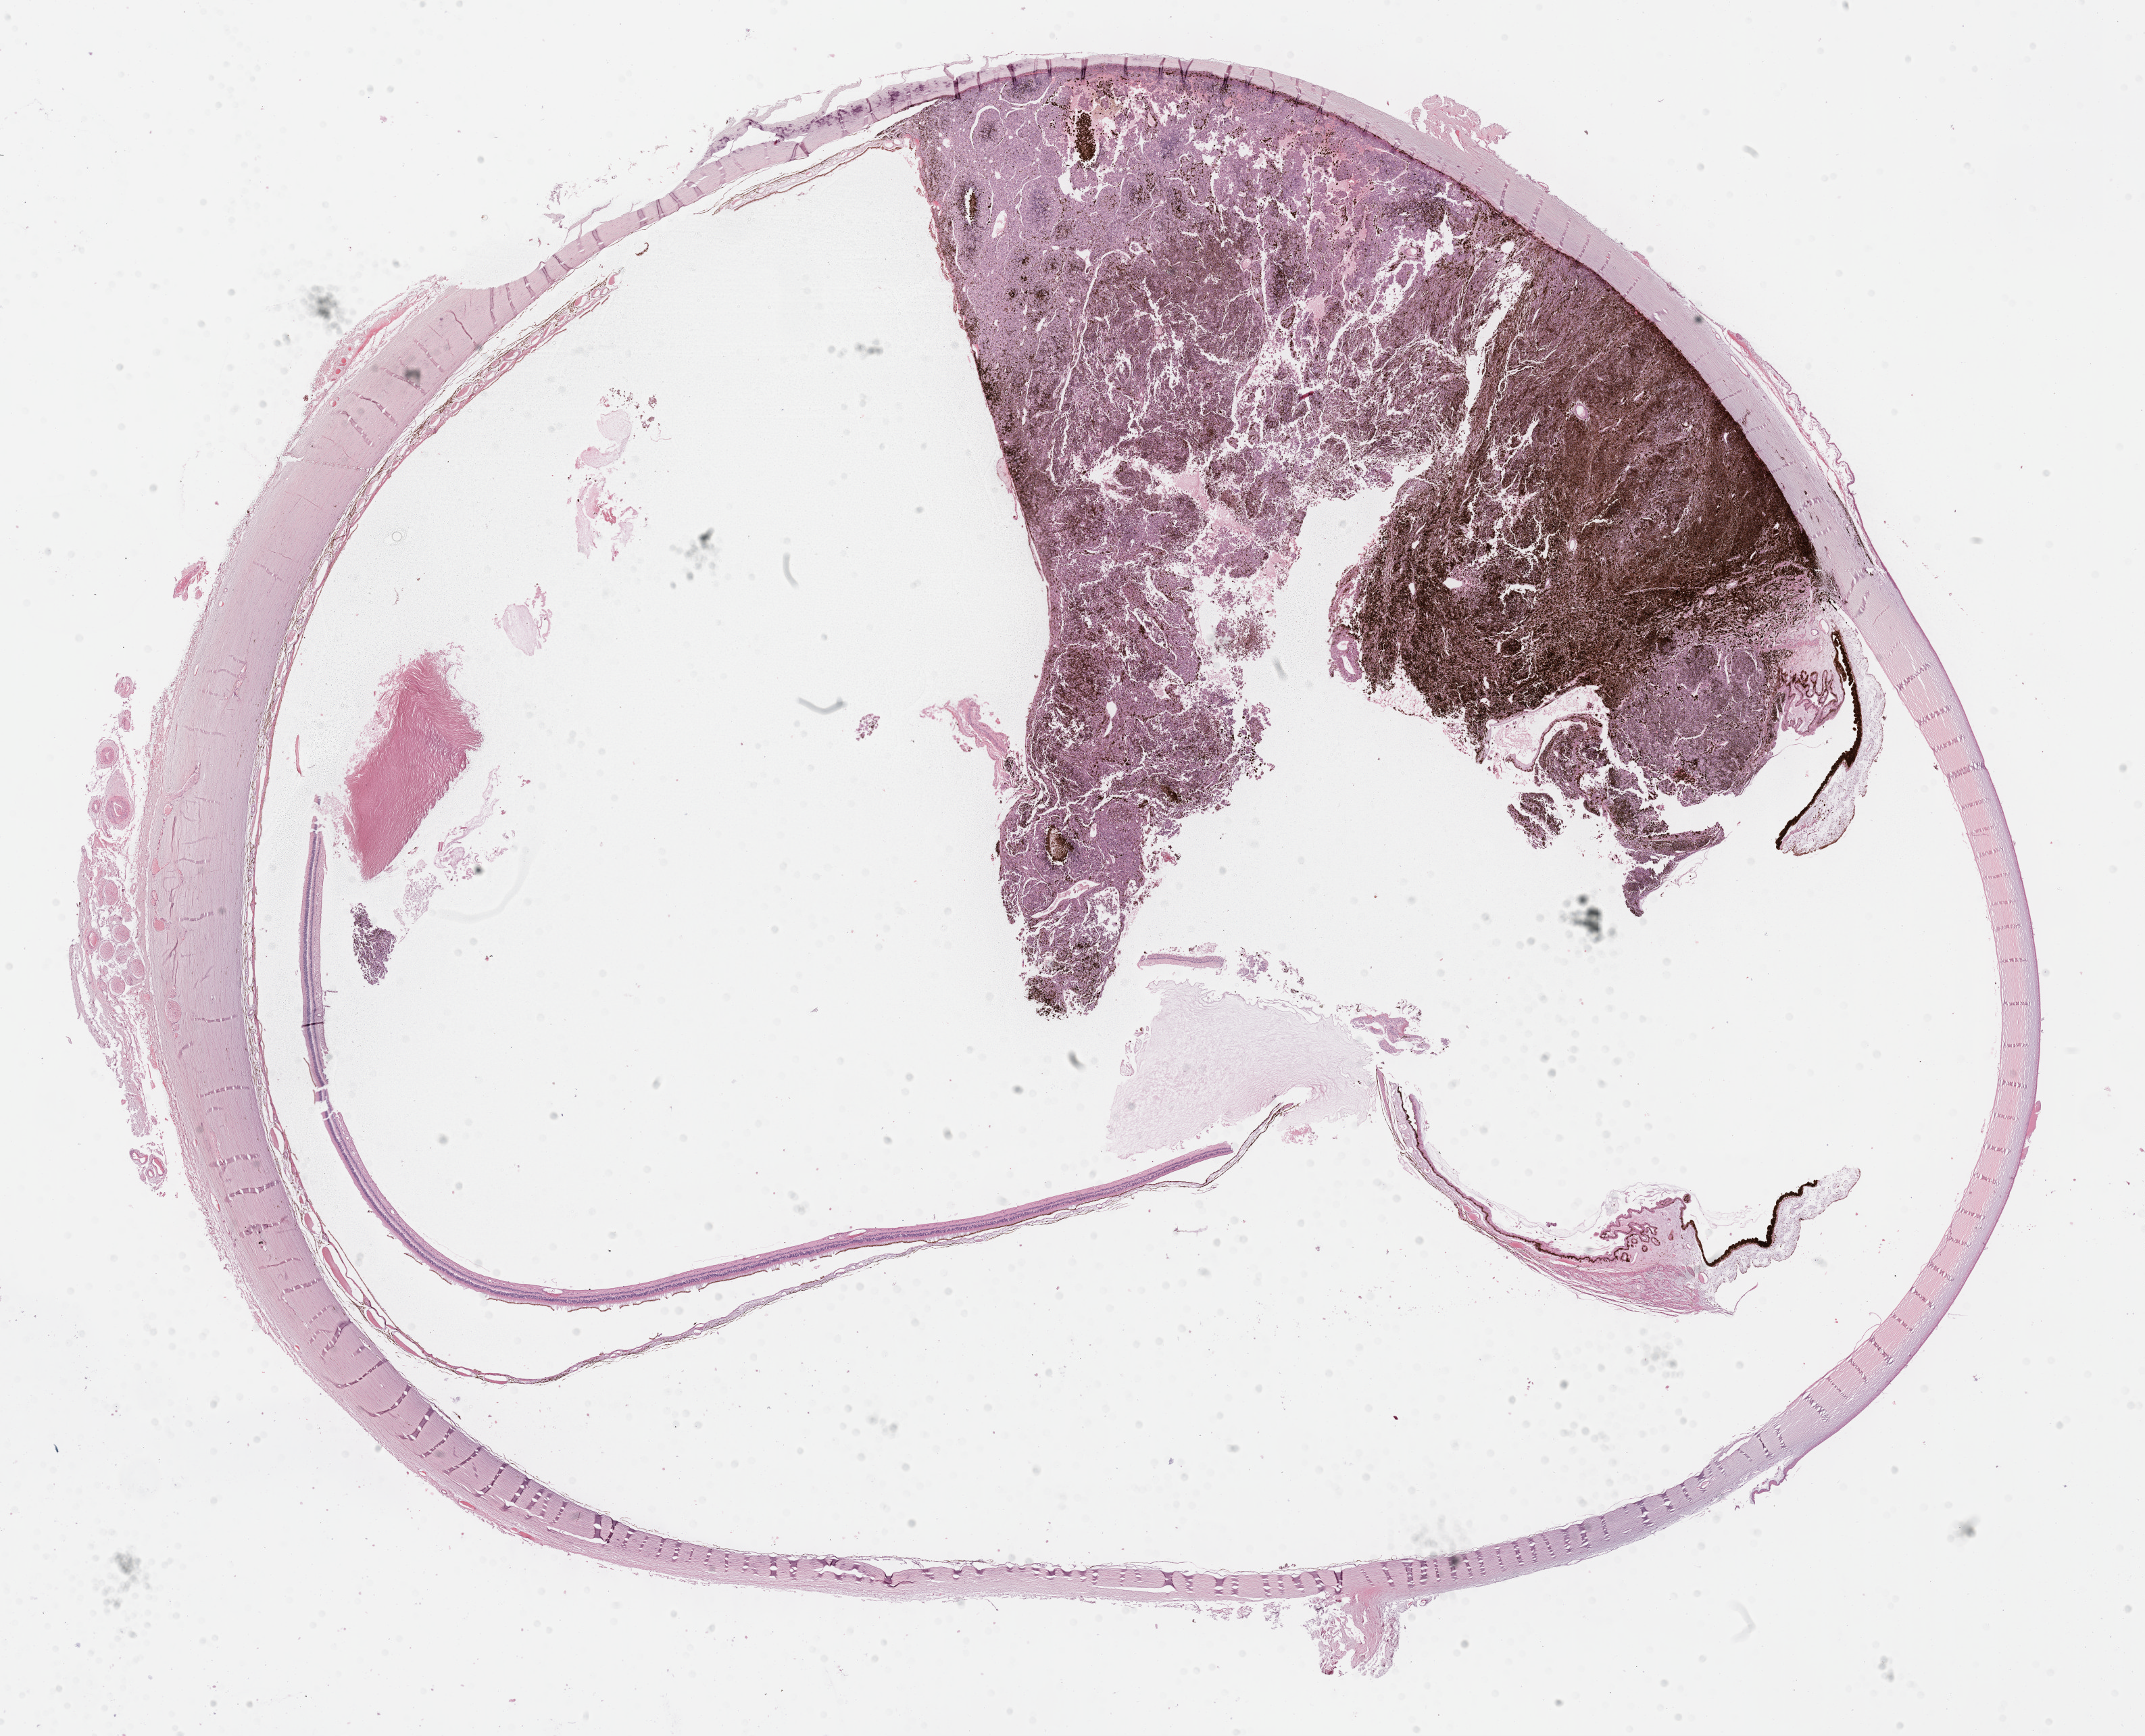
Digitized H&E tissue section (whole slide) — shown as a low-resolution overview of the whole scanned area (about 25.7 x 20.8 mm, acquisition: 40x scan). FFPE section. Primary tumour sample from the uvea. Patient: female, age at initial diagnosis 83 years.
• diagnosis: Epithelioid cell melanoma (ciliary body)
• AJCC pathologic stage: IIIC (7th edition)